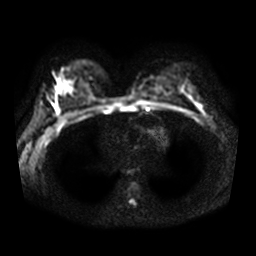
Breast MRI, one axial slice. Position 22 of 36 along the scan axis. Diffusion-weighted series; image 2 of 4 stored at this slice position (different b-values; order by instance number). 3 T. 5 mm slice thickness. 256 × 256 image matrix, field of view 340 × 340 mm. Female patient.
Structures marked on this image (expert manual segmentation):
- tumour on diffusion-weighted imaging: bounding box [x1, y1, x2, y2] px = [196, 104, 202, 108]